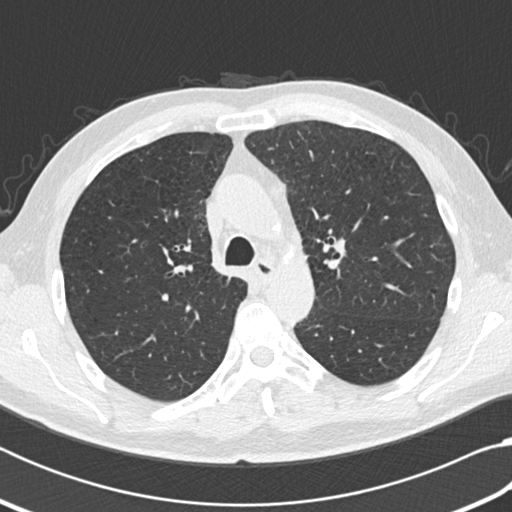
Chest CT (low-dose screening protocol), one axial image. Third screening round (two years after baseline). Lung window (W 1500 / L -600 HU). Male participant, aged 64 years at enrolment. Current smoker at enrolment.
• Expert-annotated lung lesion, bounding box <252,177,287,213> (left, top, right, bottom; pixels).
• Screening reader's record for this exam: no non-calcified nodule ≥4 mm recorded.
• Lung cancer was diagnosed 163 days after this screen: small cell carcinoma, NOS, mediastinum, stage IV (AJCC 6th edition).